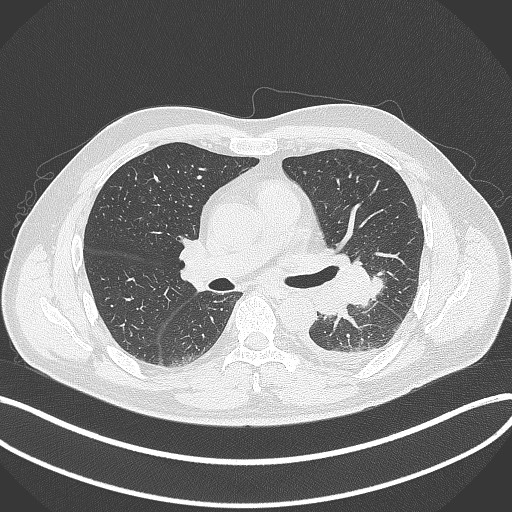
Chest CT, one axial slice; slice 206 of 342 in the series (ordered by position); lung window (W 1500 / L -600 HU); 512 × 512 image matrix. Male patient, age 58 years. Case-level facts recorded for this patient, not image findings: clinical TNM (as recorded): T3 N1 M1b.
Outlined on this slice (rectangle marked by the reading radiologist):
- lung tumour (recorded histology: small cell carcinoma): box from (x=344, y=255) to (x=381, y=310) px